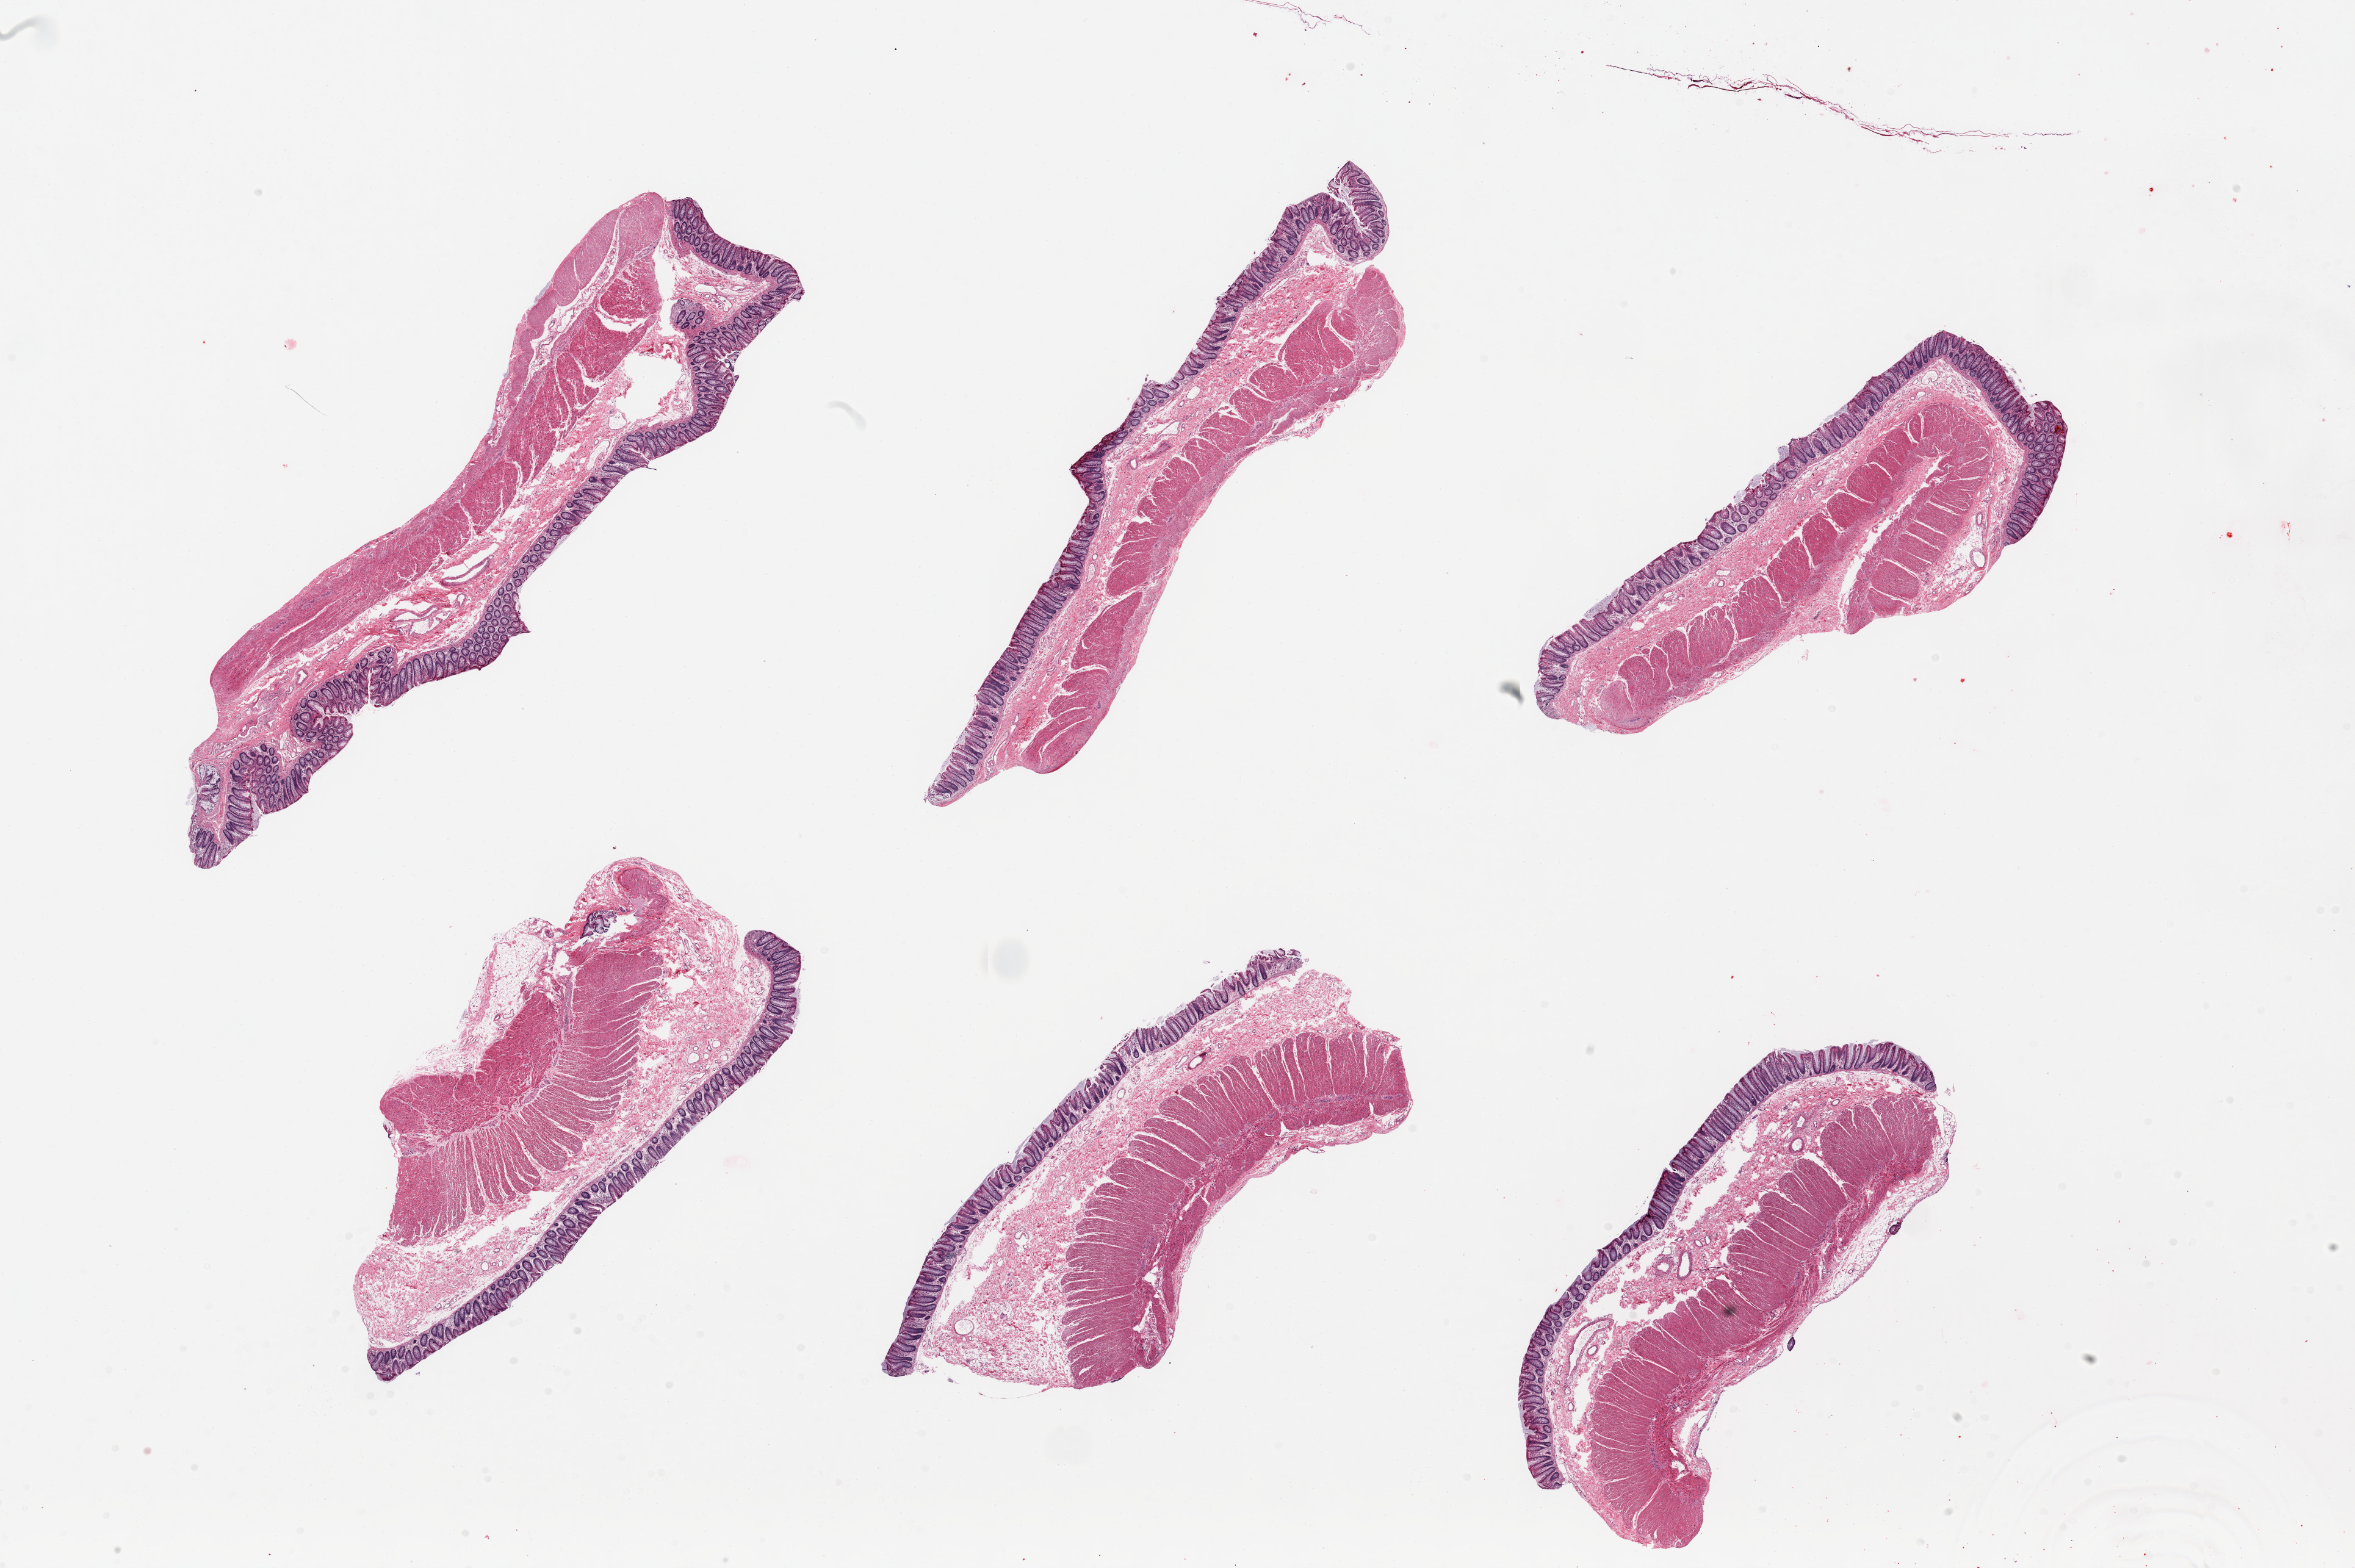
H&E whole-slide image, brightfield, whole scanned area (about 30.5 x 20.3 mm) shown as a low-resolution overview, PAXgene-fixed, paraffin-embedded tissue, sampled site (target tissue): transverse colon, tissue donor sample. Donor sex: male.
Review note (as recorded): 6 pieces; full thickness sections.